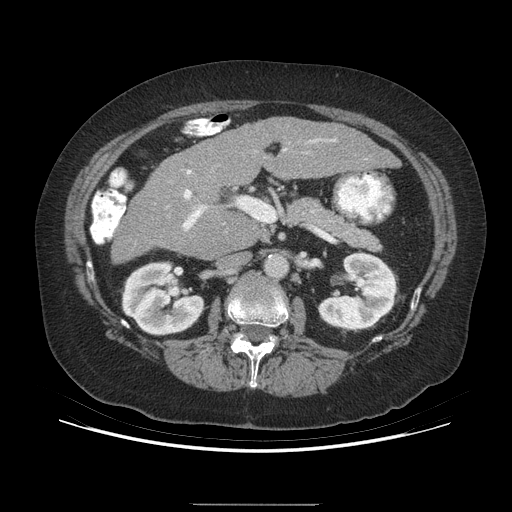
Contrast-enhanced abdominal CT (liver protocol), one axial slice; position 143 of 192 along the scan axis; reconstruction kernel STANDARD; soft-tissue window (W 400 / L 40 HU); 512 × 512 image matrix, field of view 400 × 400 mm. Case-level facts recorded for this patient, not image findings: diagnosis: hepatocellular carcinoma (patient treated with transarterial chemoembolisation; whether this scan precedes or follows treatment is not stated here); TNM stage (as recorded): Stage-I; Child-Pugh class: A; tumour differentiation: moderately differentiated; tumour nodularity: uninodular.
Annotated regions visible in this slice (semi-automatically segmented with operator editing):
- liver parenchyma outside the tumour (the mass and vessels are separate outlines, so this box may not span the whole liver): bounding box [x1, y1, x2, y2] px = [110, 118, 396, 263]
- liver vessels: [184, 139, 335, 199]